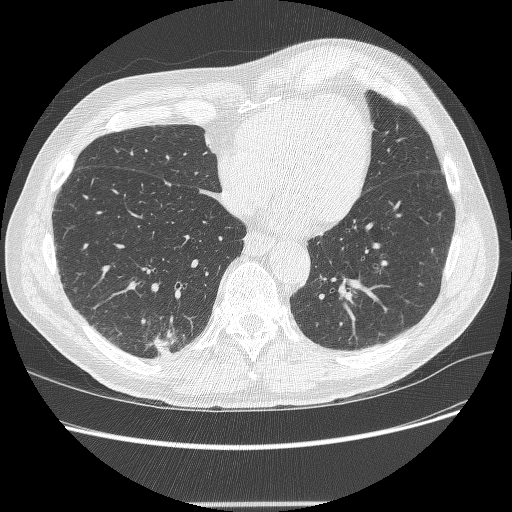
Axial slice from a low-dose chest CT screening exam; second annual screen; lung window (W 1500 / L -600 HU); 1.25 mm slice thickness. Male participant, aged 71 years at enrolment. Current smoker at enrolment.
Expert reader's lesion annotation, bounding box <137,323,190,365> (left, top, right, bottom; pixels). The screening reader recorded 5 non-calcified nodules or masses ≥4 mm on this exam (right lower lobe, right lower lobe, right upper lobe, right upper lobe, right upper lobe); which of them this box marks is not recorded. Later outcome: lung cancer diagnosed 7 days after this screen — squamous cell carcinoma, NOS, right lower lobe, moderately differentiated (G2), stage IA (AJCC 6th edition), 27 mm at pathology.